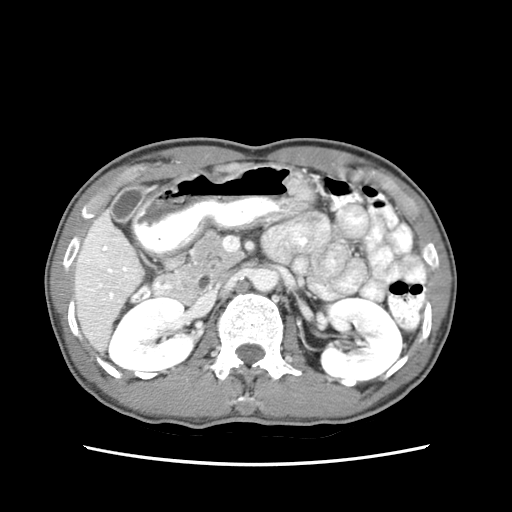
Contrast-enhanced abdominal CT (liver protocol), one axial slice. Slice 26 of 79 in the series (ordered by position). Reconstruction kernel STANDARD. Soft-tissue window (W 400 / L 40 HU). 2.5 mm slice thickness. 512 × 512 image matrix, field of view 320 × 320 mm. Case-level facts recorded for this patient, not image findings: diagnosis: hepatocellular carcinoma (patient treated with transarterial chemoembolisation; whether this scan precedes or follows treatment is not stated here); TNM stage (as recorded): Stage-IIIB; Child-Pugh class: A; tumour differentiation: moderately differentiated.
Structures marked on this image (semi-automatic segmentation, software-assisted and operator-edited):
- liver parenchyma outside the tumour (the mass and vessels are separate outlines, so this box may not span the whole liver): bounding box (x1, y1, x2, y2) in pixels: (74, 210, 140, 348)
- liver vessels: (83, 211, 137, 300)